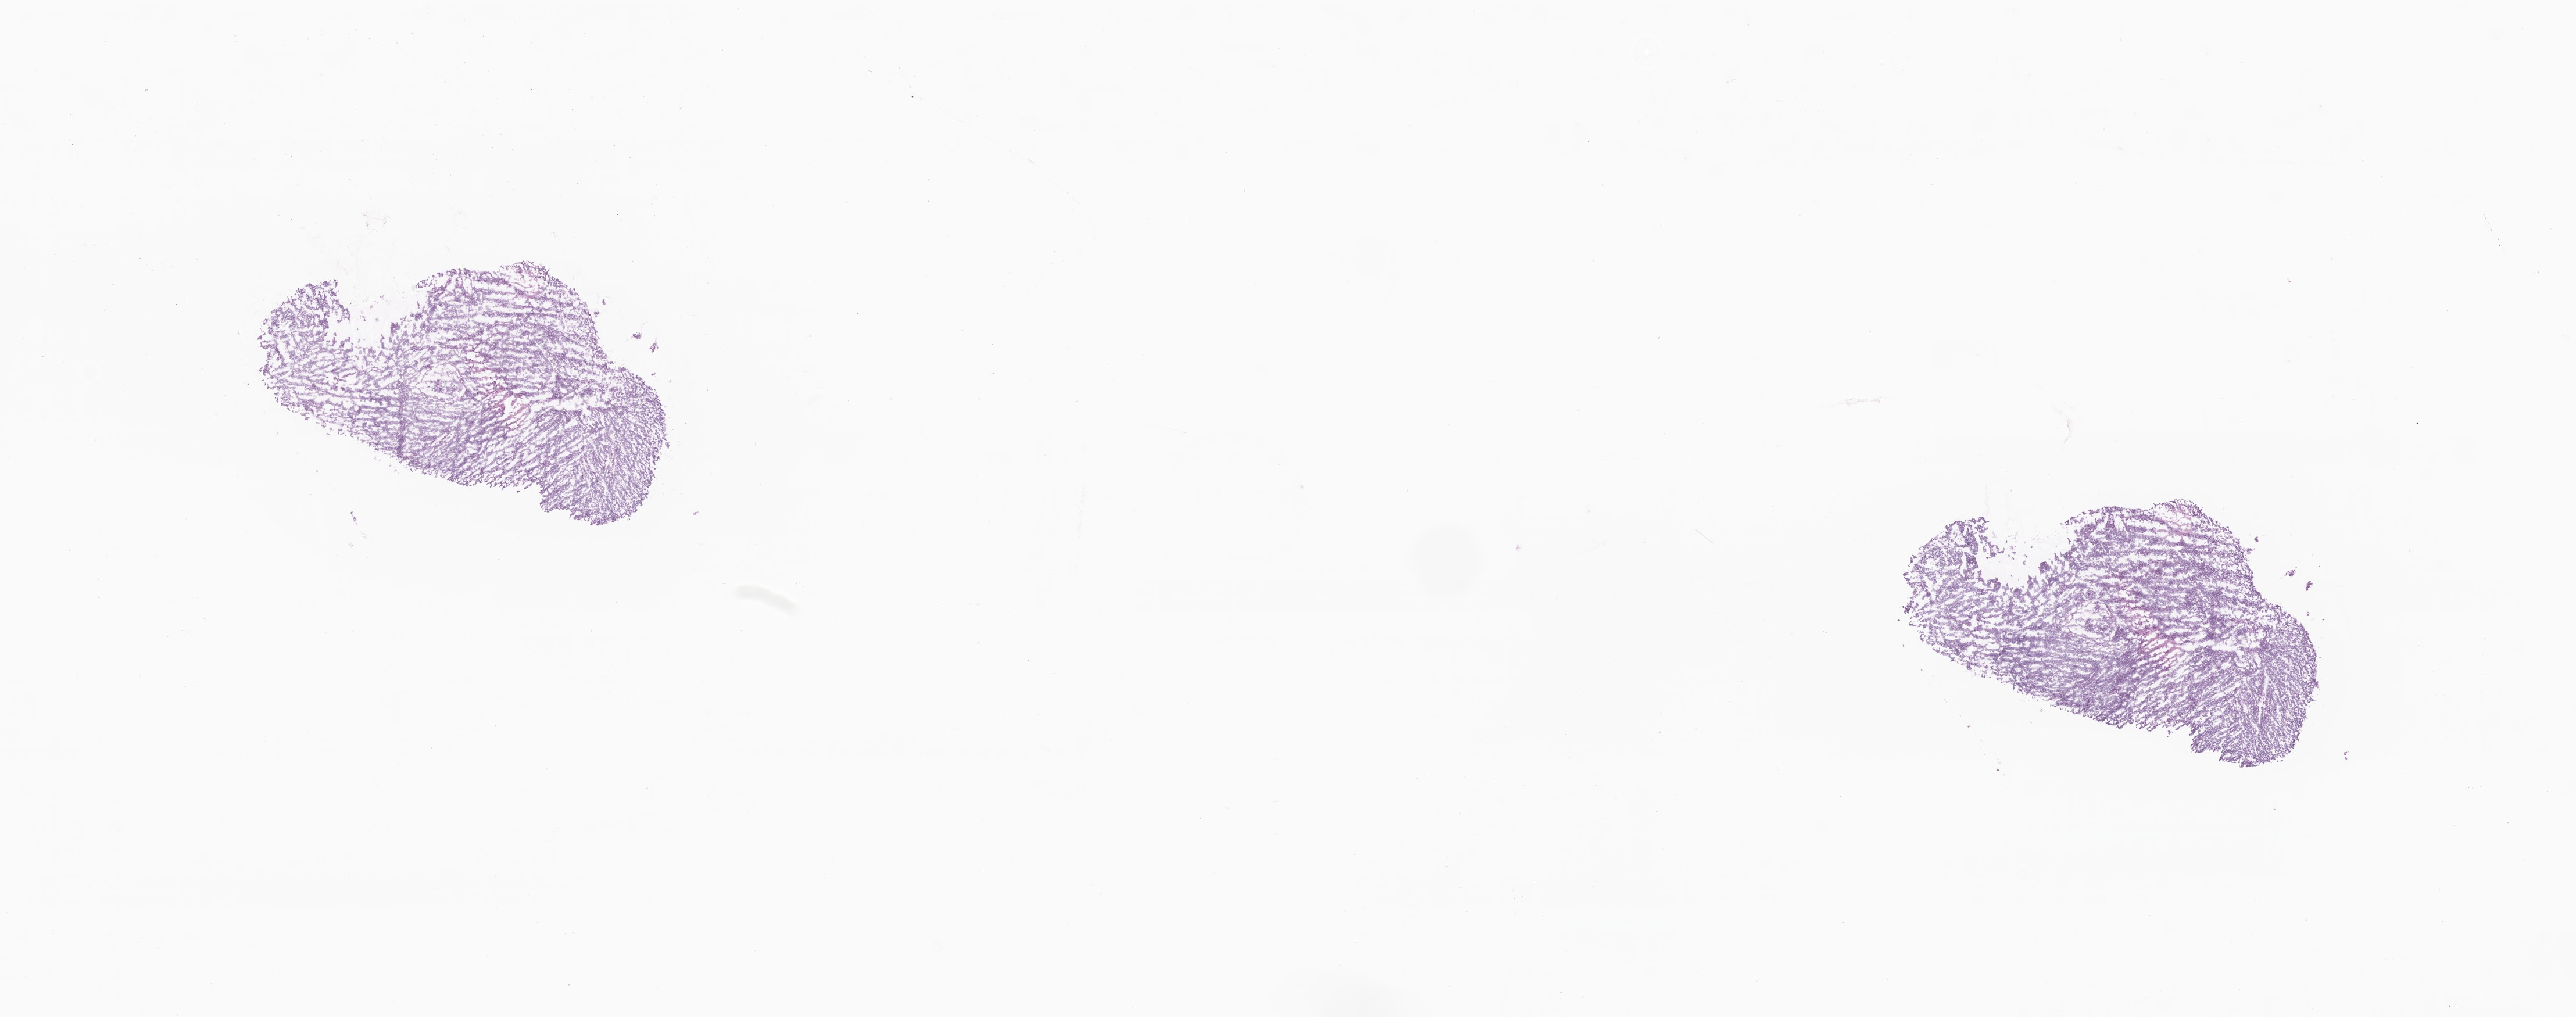
Digitized haematoxylin and eosin-stained section — whole scanned area (about 18.7 x 7.4 mm) shown as a low-resolution overview. Cryosection. Primary tumor. Anatomic site: body of uterus. Female patient. Tumor grade: G3 (poorly differentiated). Composition of this section per pathologist review: tumor cells 80%, tumor nuclei 80%, stromal cells 20%, necrosis 0%, normal cells 0%. Inflammatory infiltration, as recorded: lymphocyte infiltration 0%, monocyte infiltration 0%, neutrophil infiltration 0%.
• AJCC pathologic stage: Stage IB
• diagnosis: Carcinoma, undifferentiated, NOS